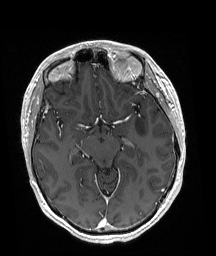
Brain MRI from a brain-tumour surgery series, one axial slice; slice 113 of 192 in the series (ordered by position); T1-weighted post-contrast; 1 mm slice thickness; 216 × 256 image matrix, field of view 211 × 250 mm. Case-level facts recorded for this patient, not image findings: histopathology: Astrocytoma; WHO grade: 3; IDH mutation: yes; tumour location: Left Posterior Frontal.
Annotated regions visible in this slice (outlined manually by an expert reader):
- tumour: bounding box [x1, y1, x2, y2] px = [135, 117, 147, 139]